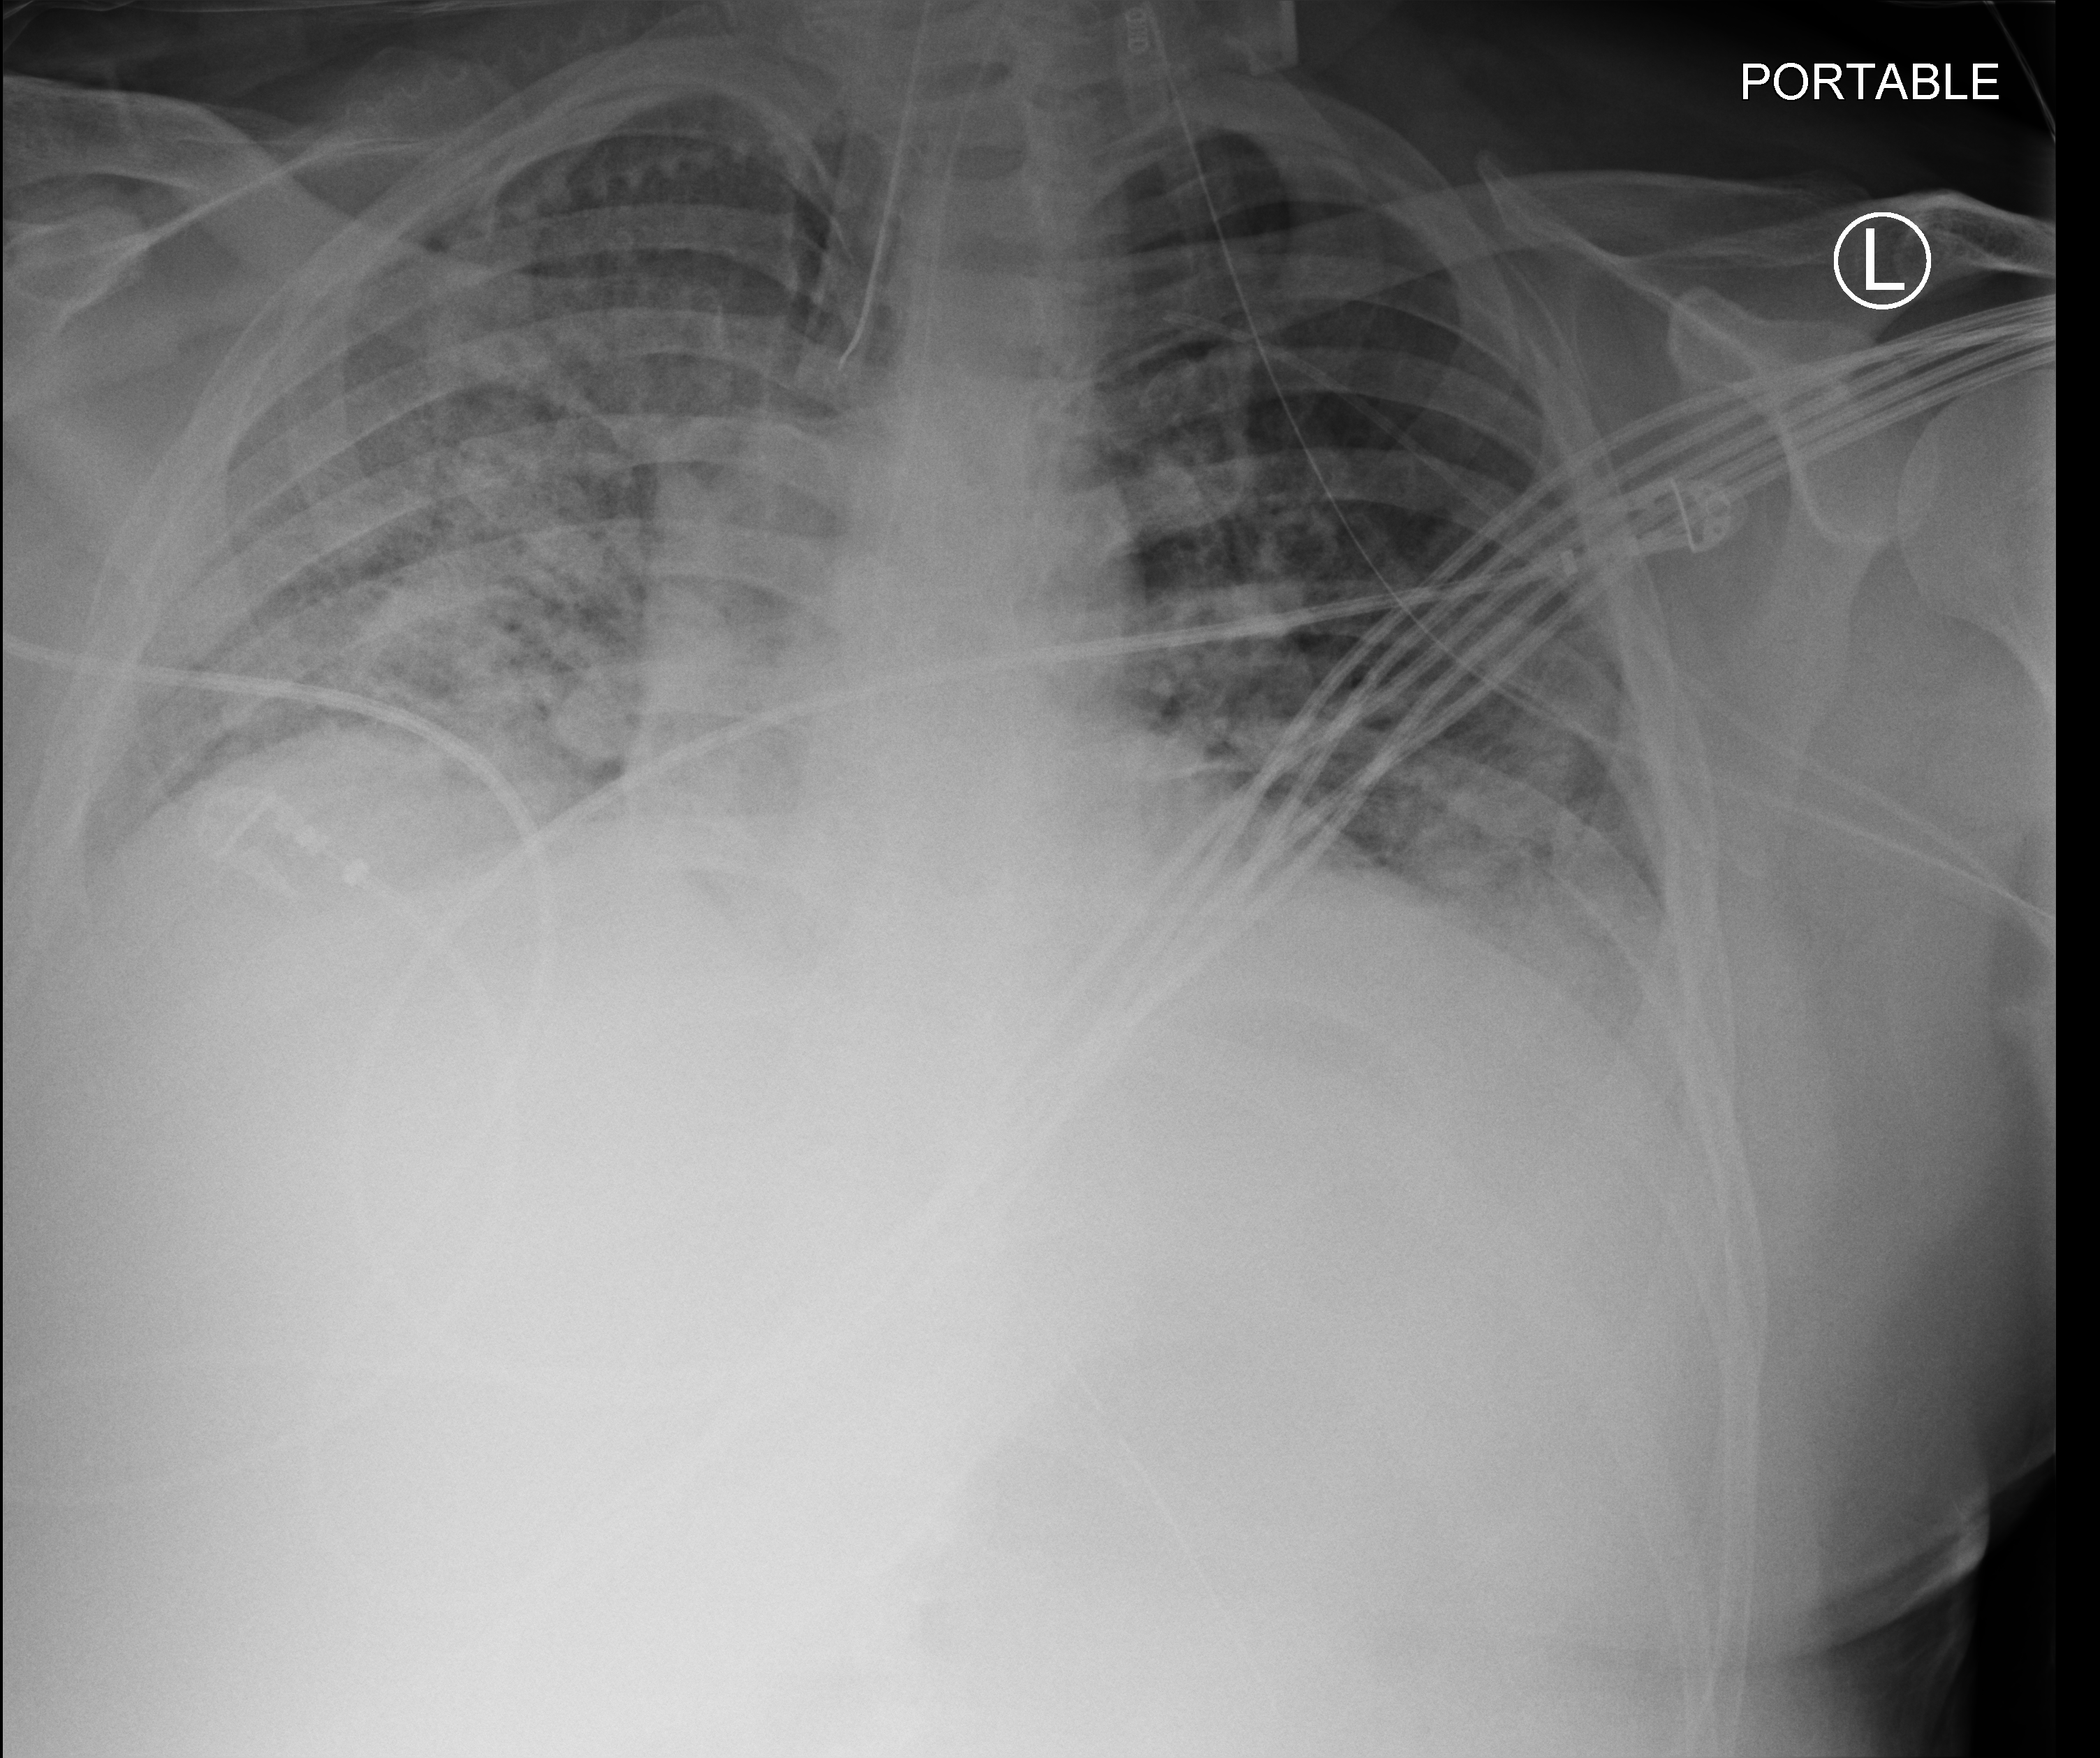
Chest X-ray (portable); anteroposterior (AP) projection. Male patient hospitalised with COVID-19, age 18–59 years.
Admission-level facts for this patient (not findings on this image; timing relative to this image not recorded): other chronic lung disease (admission record): no.